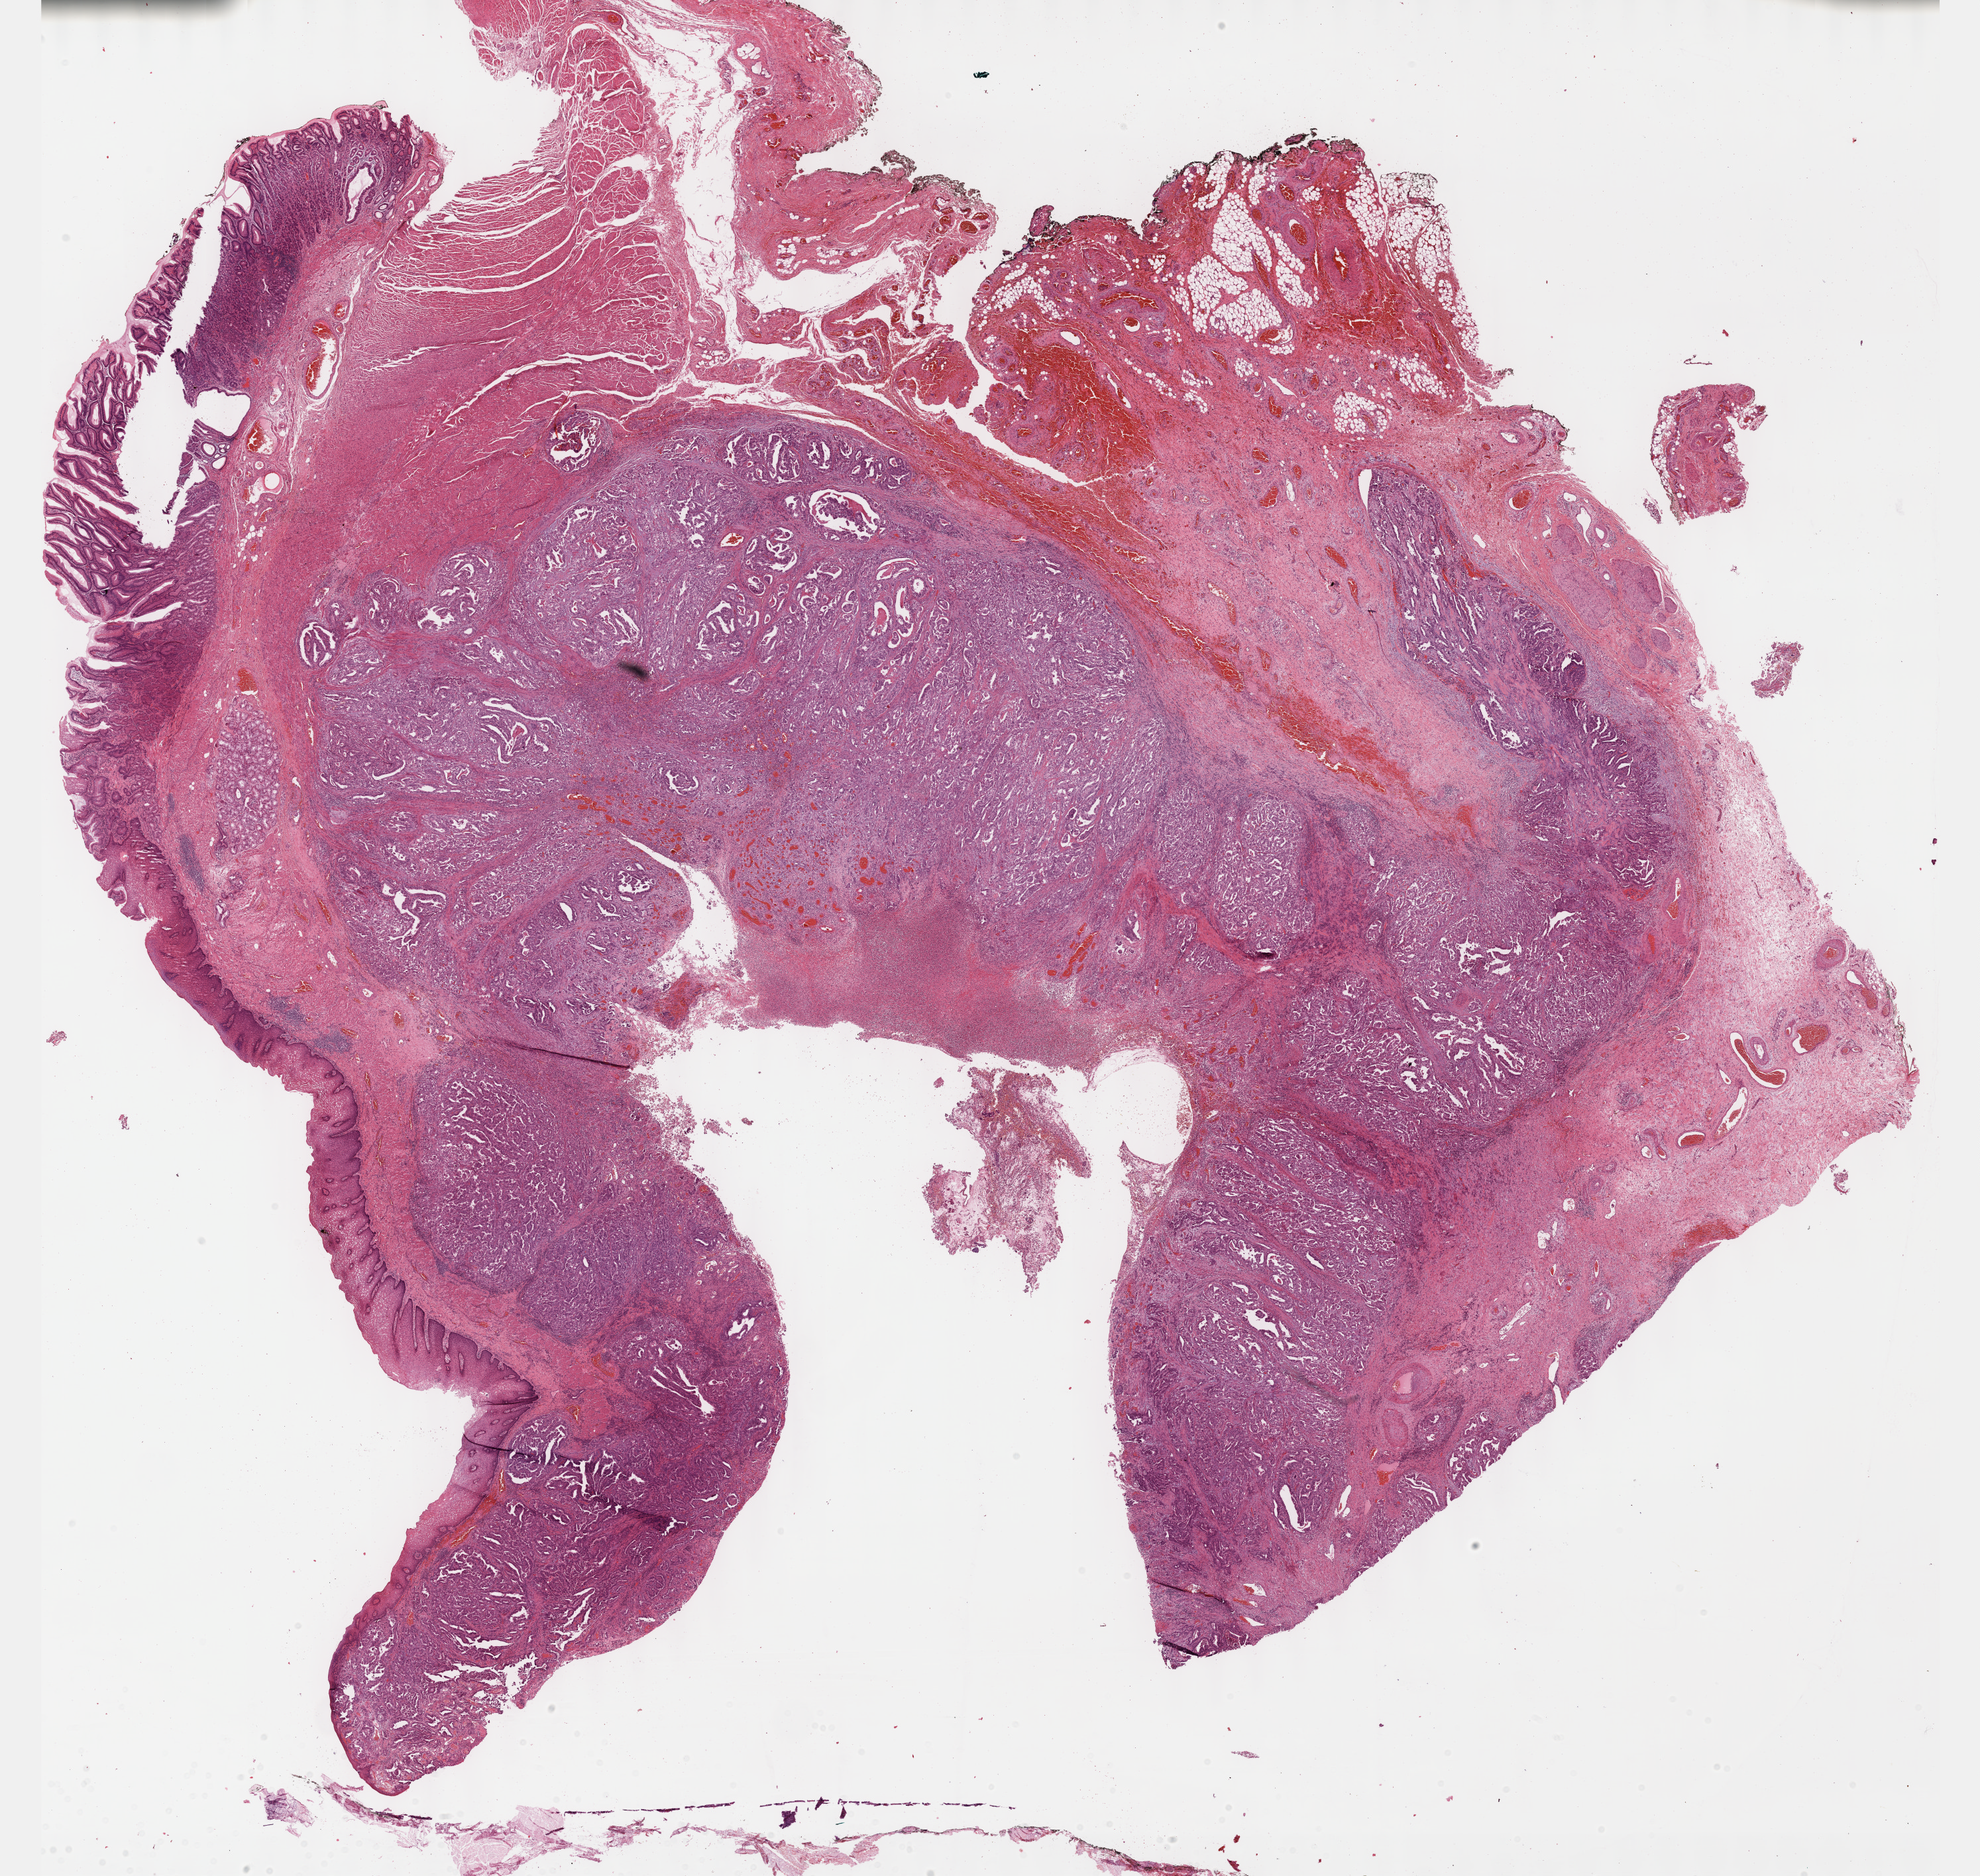
H&E-stained whole-slide image, a low-resolution overview of the entire scanned area, about 24.1 x 22.9 mm (from a 40x scan). Formalin-fixed paraffin-embedded (FFPE) diagnostic section. Sample: primary tumour, stomach. Male, age 58 years at initial diagnosis. Histologic grade: G2 (moderately differentiated).
Lymph nodes positive (case pathology): 11 of 32 examined. AJCC pathologic stage: IIIB (7th edition). Pathologic diagnosis: Adenocarcinoma, intestinal type (cardia, NOS).